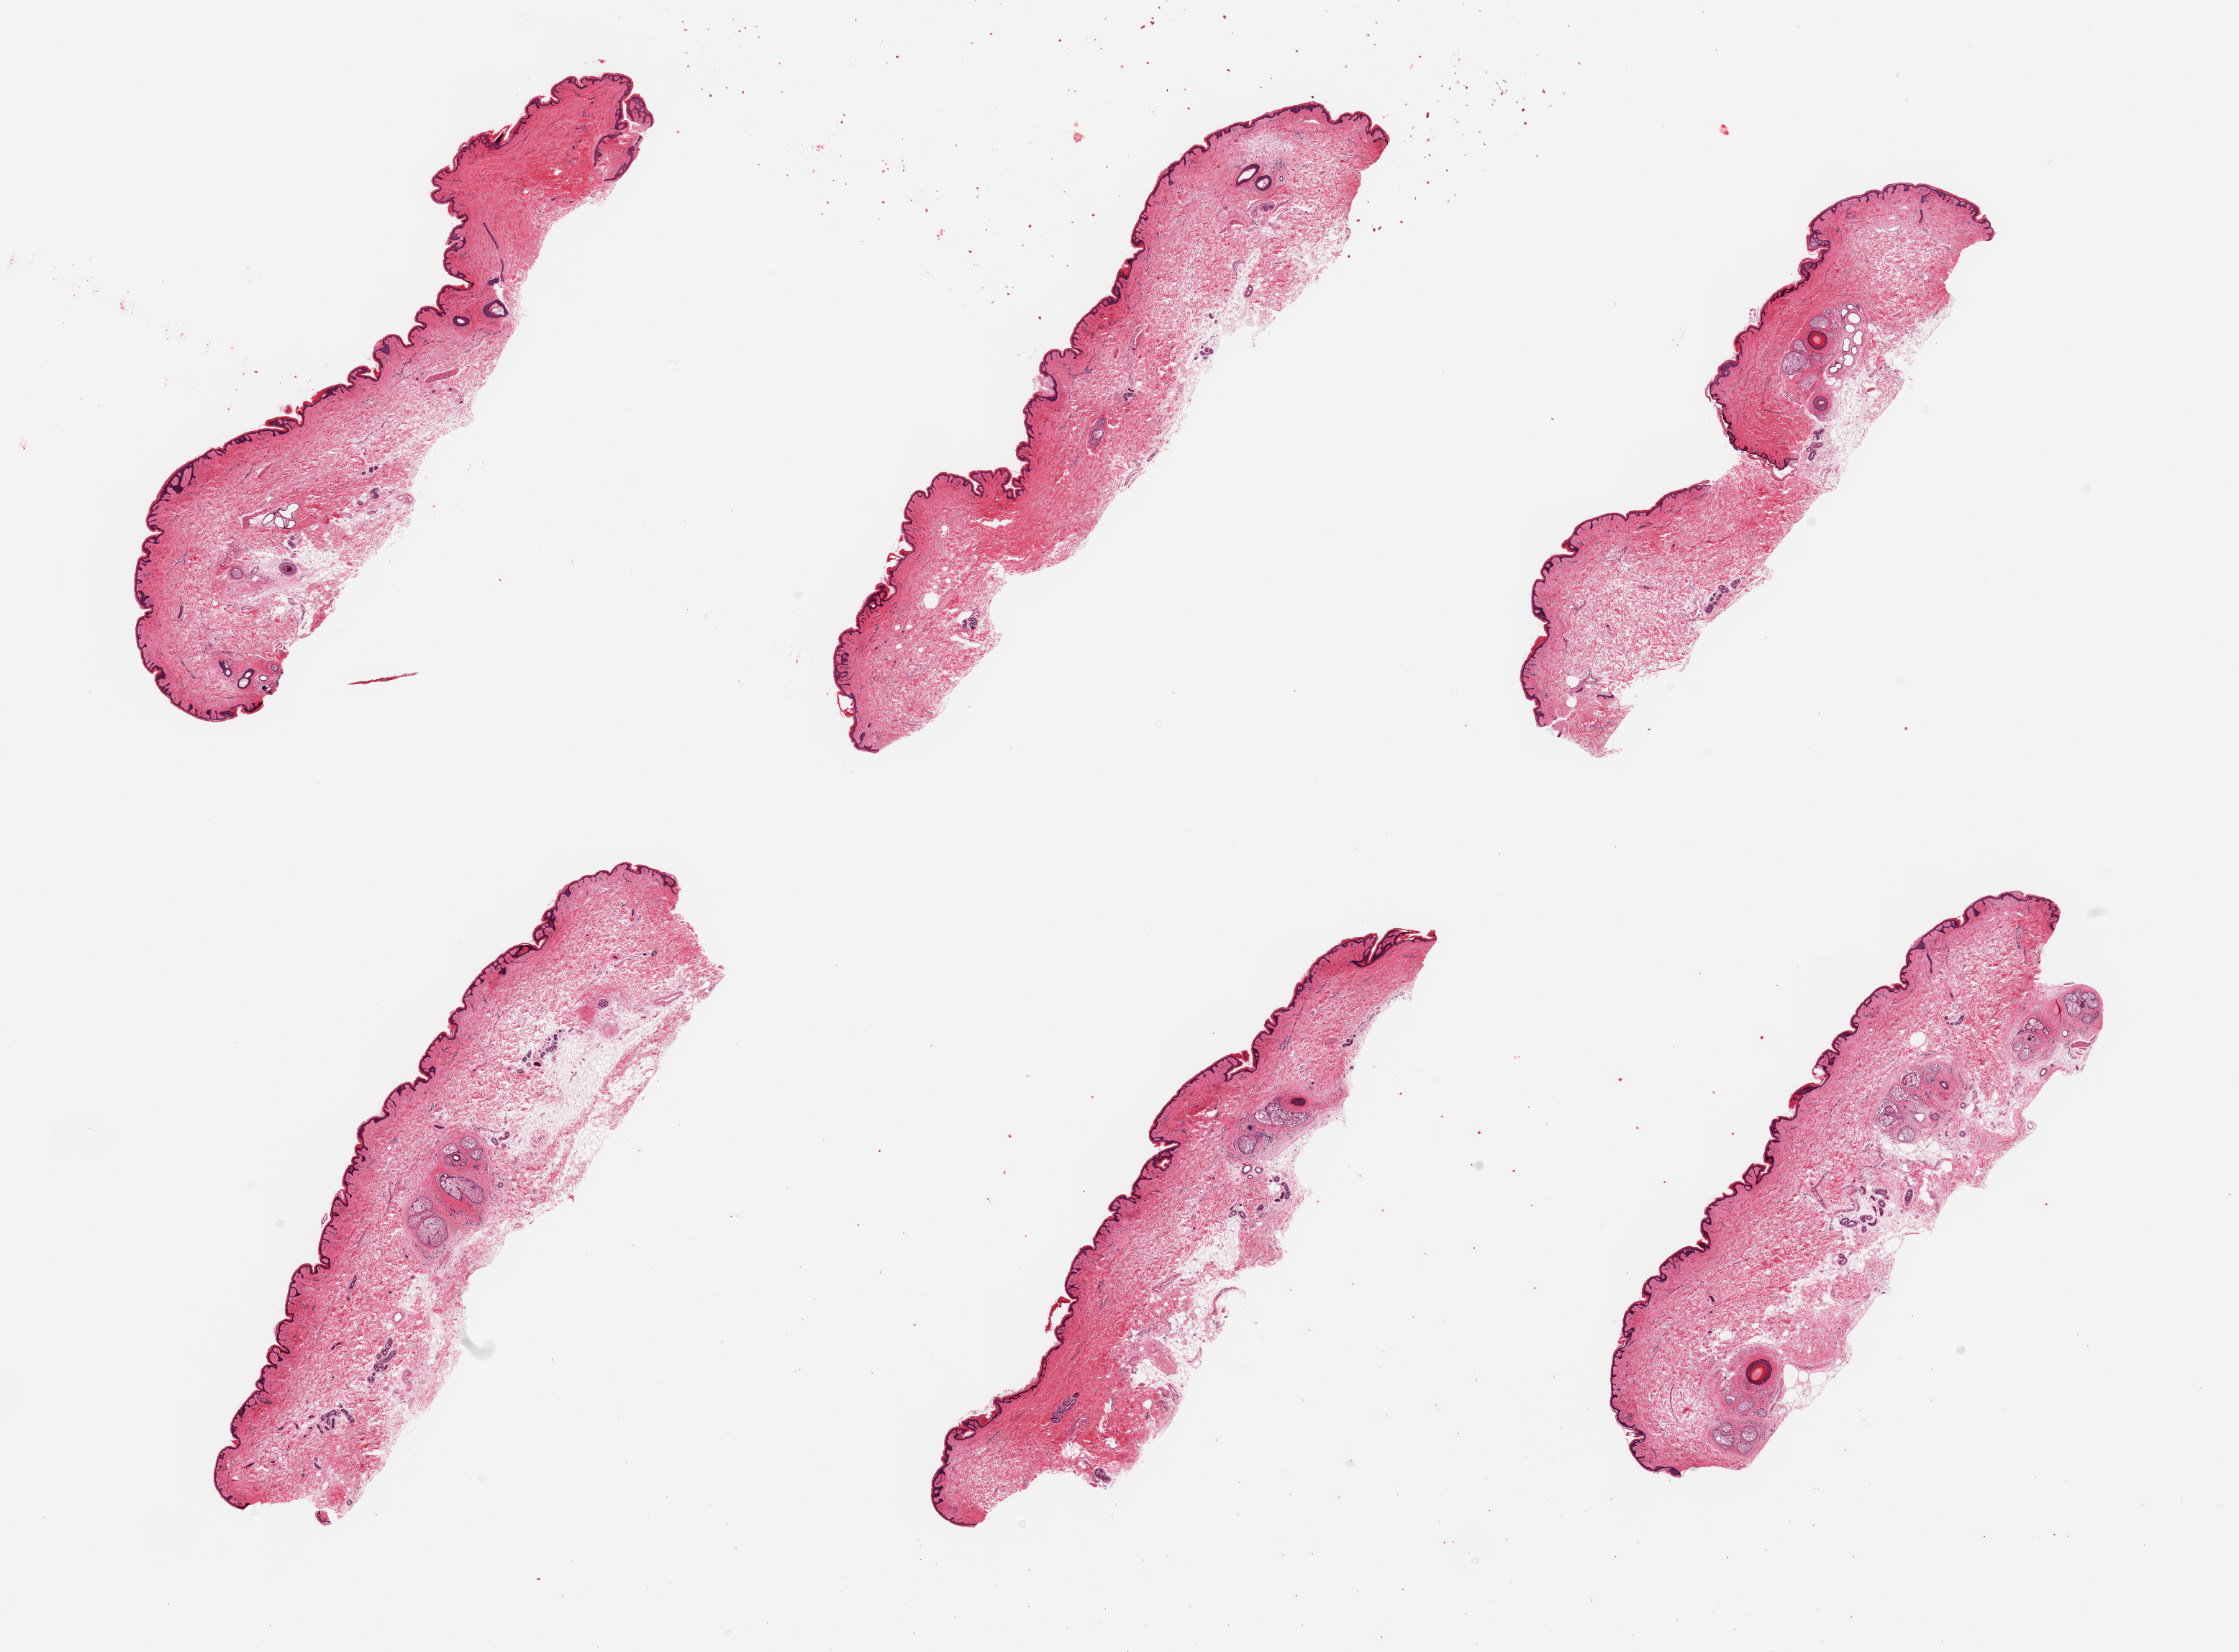
Whole-slide image, haematoxylin and eosin stain, brightfield — whole scanned area (about 24.6 x 18.2 mm) shown as a low-resolution overview. PAXgene-fixed paraffin-embedded (PFPE) section. Sampled site (target tissue): skin of suprapubic region. Donor tissue sample.
Pathologist's review note for this sample: 6 pieces; well trimmed; 10% dermal fat.